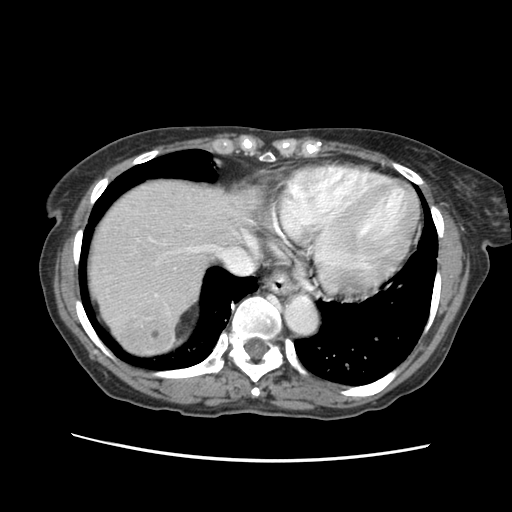
Contrast-enhanced abdominal CT (liver protocol), one axial slice; slice 52 of 63 in the series (ordered by position); reconstruction kernel STANDARD; 120 kVp; soft-tissue window (W 400 / L 40 HU); 512 × 512 image matrix, field of view 340 × 340 mm. From the clinical record (not read from this slice): diagnosis: hepatocellular carcinoma (patient treated with transarterial chemoembolisation; whether this scan precedes or follows treatment is not stated here); TNM stage (as recorded): Stage-I; Child-Pugh class: B; tumour differentiation: well differentiated.
Structures marked on this image (semi-automatic segmentation, software-assisted and operator-edited):
- liver parenchyma outside the tumour (the mass and vessels are separate outlines, so this box may not span the whole liver): bounding box <90,180,250,352> (left, top, right, bottom; pixels)
- mass: <115,311,169,351>
- liver vessels: <153,243,212,339>